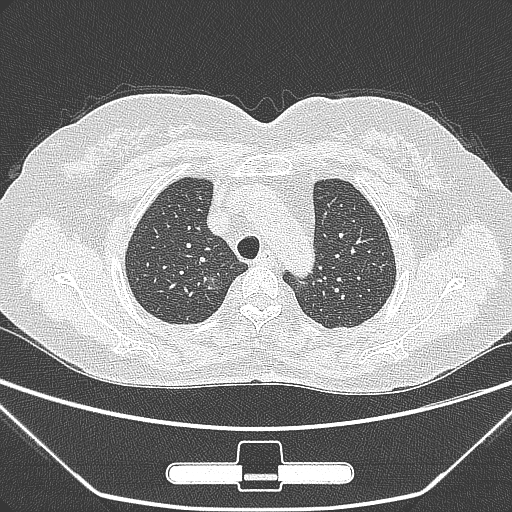
Chest CT, one axial slice. Slice 224 of 275 in the series (ordered by position). Lung window (W 1500 / L -600 HU). 1 mm slice thickness. 512 × 512 image matrix, field of view 356 × 356 mm. Patient: female, 63 years. Case-level facts recorded for this patient, not image findings: clinical TNM (as recorded): T1a N0 M0; histopathological grade: G1.
Outlined on this slice (bounding box drawn by a radiologist):
- lung tumour (recorded histology: adenocarcinoma): bounding box <197,266,226,304> (left, top, right, bottom; pixels)